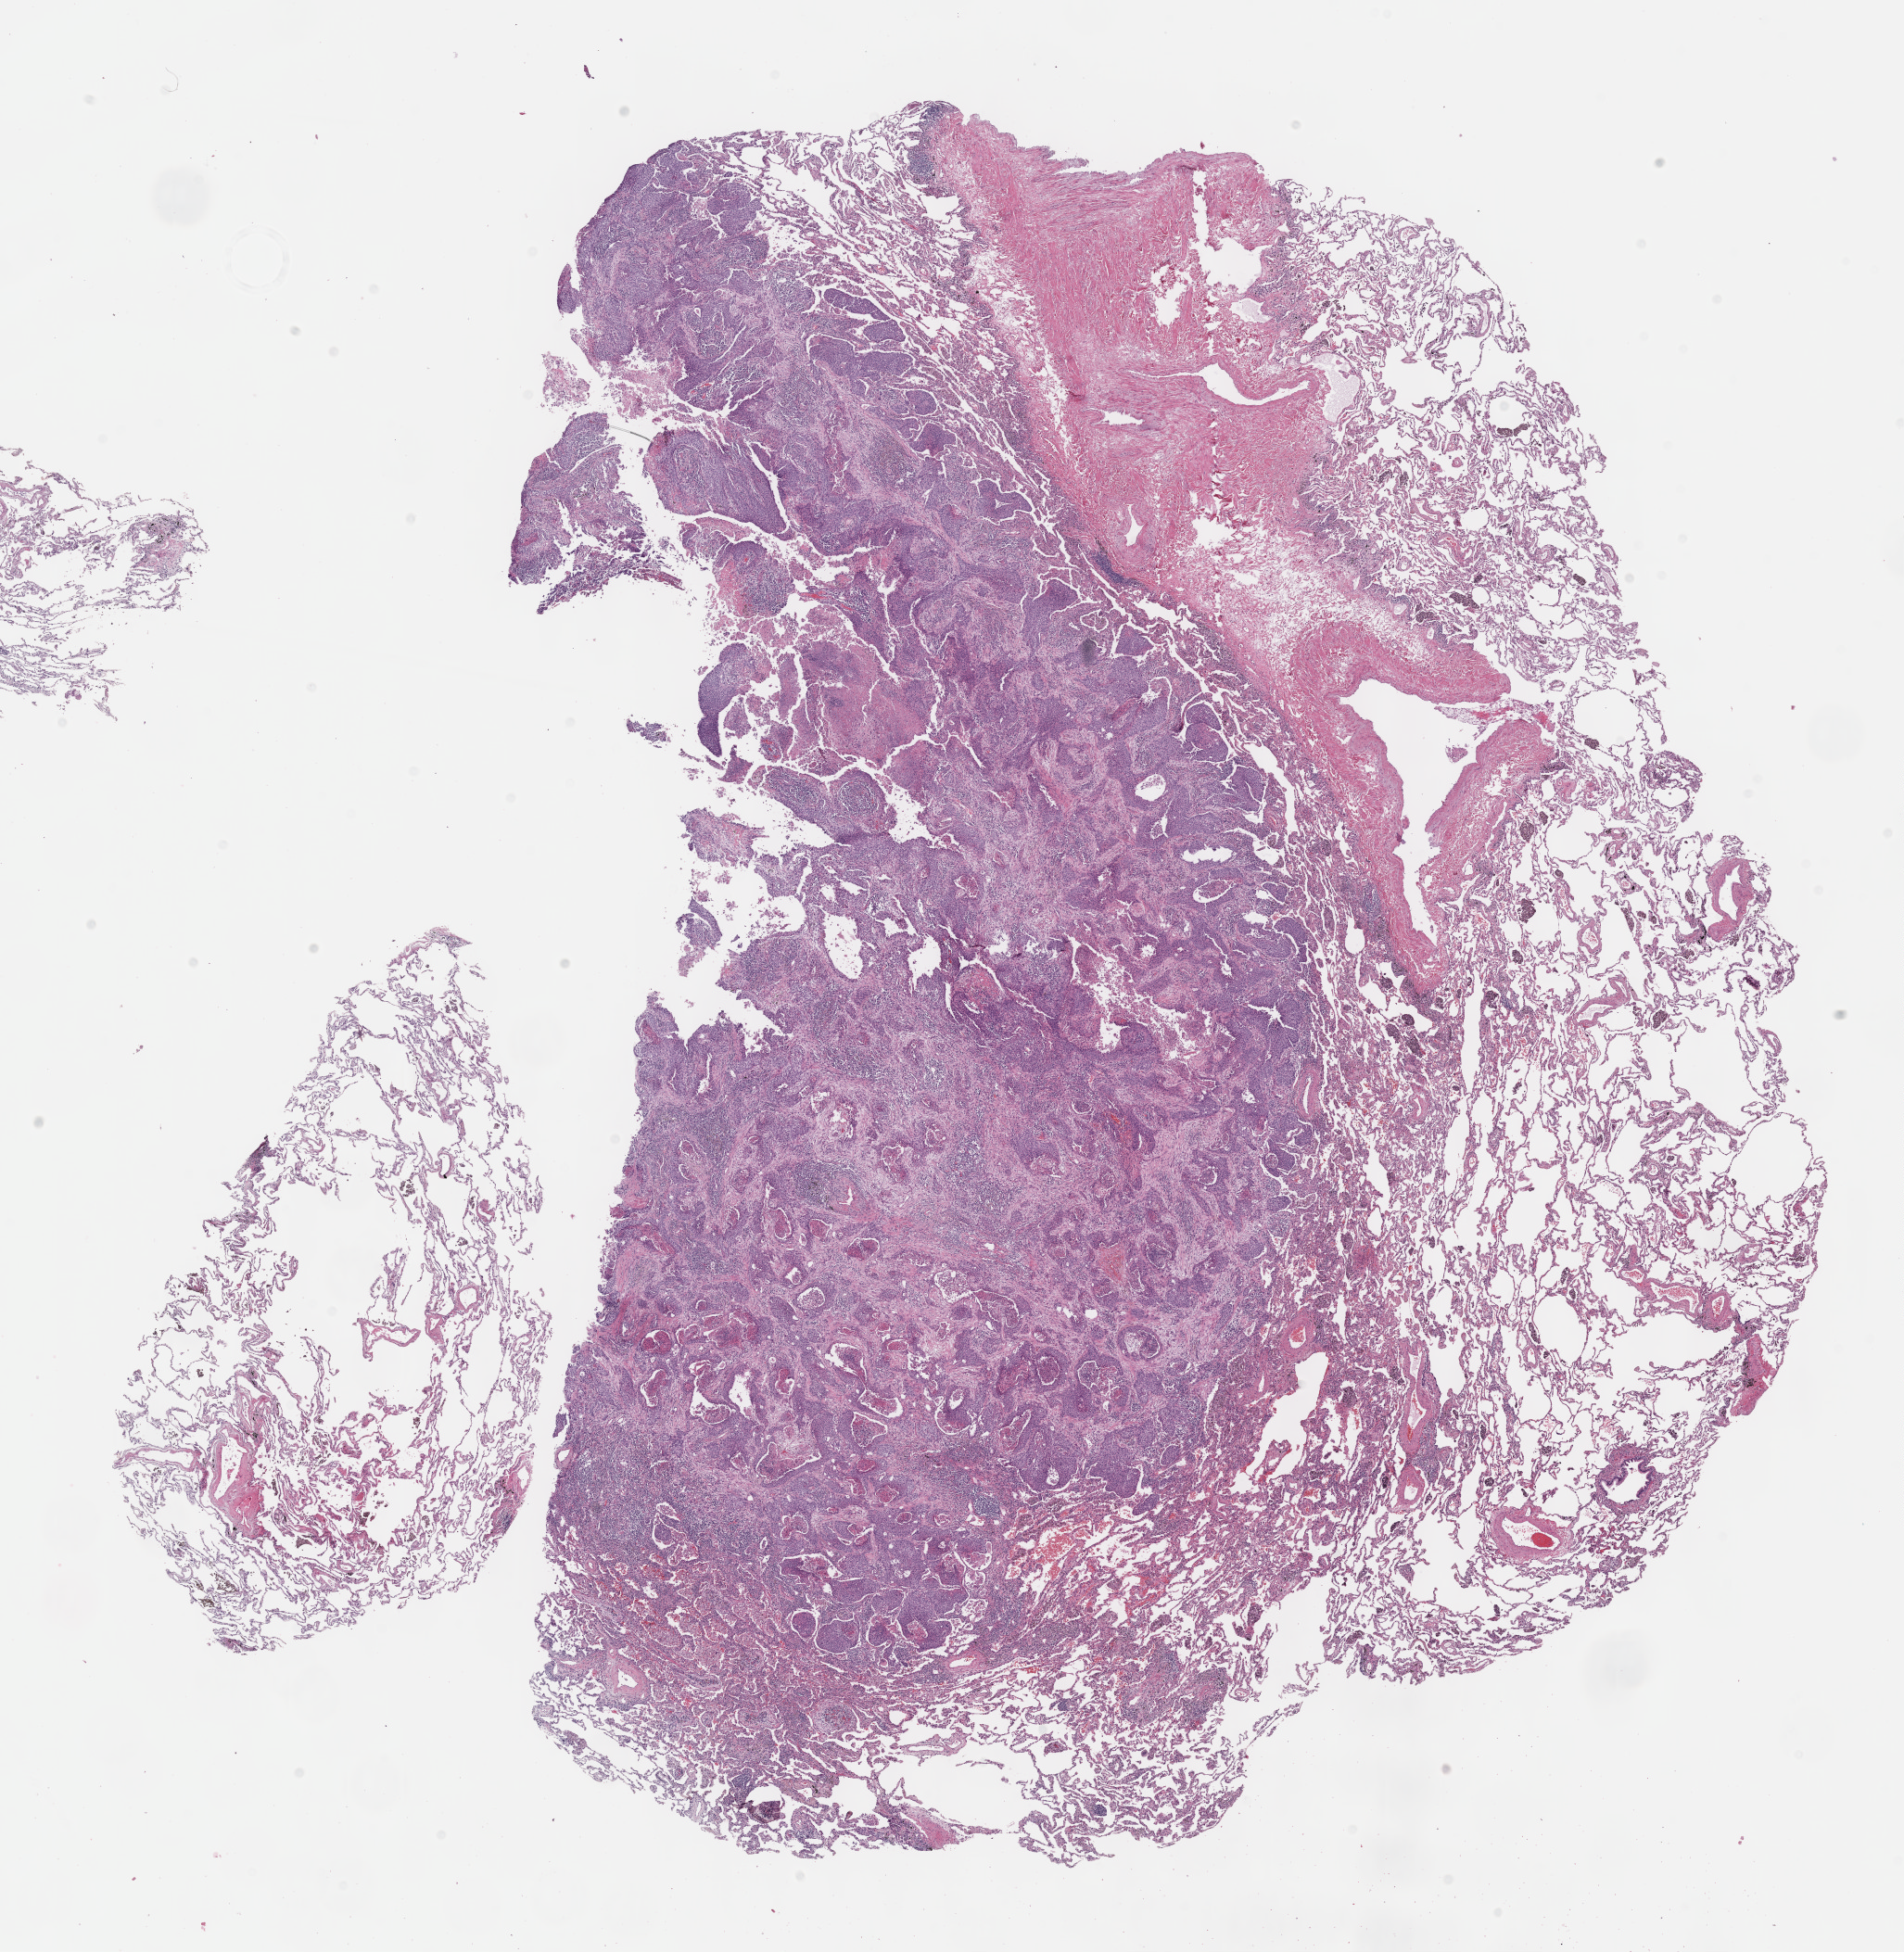
Whole-slide histology image, H&E — whole scanned area (about 16.6 x 17.0 mm, acquisition: 40x scan) shown as a low-resolution overview. Formalin-fixed paraffin-embedded (FFPE) diagnostic section. Sample: primary tumour, lung. Patient: male, age at initial diagnosis 81 years.
- AJCC pathologic stage: IA (6th edition)
- pathologic diagnosis: Squamous cell carcinoma, NOS (upper lobe, lung)